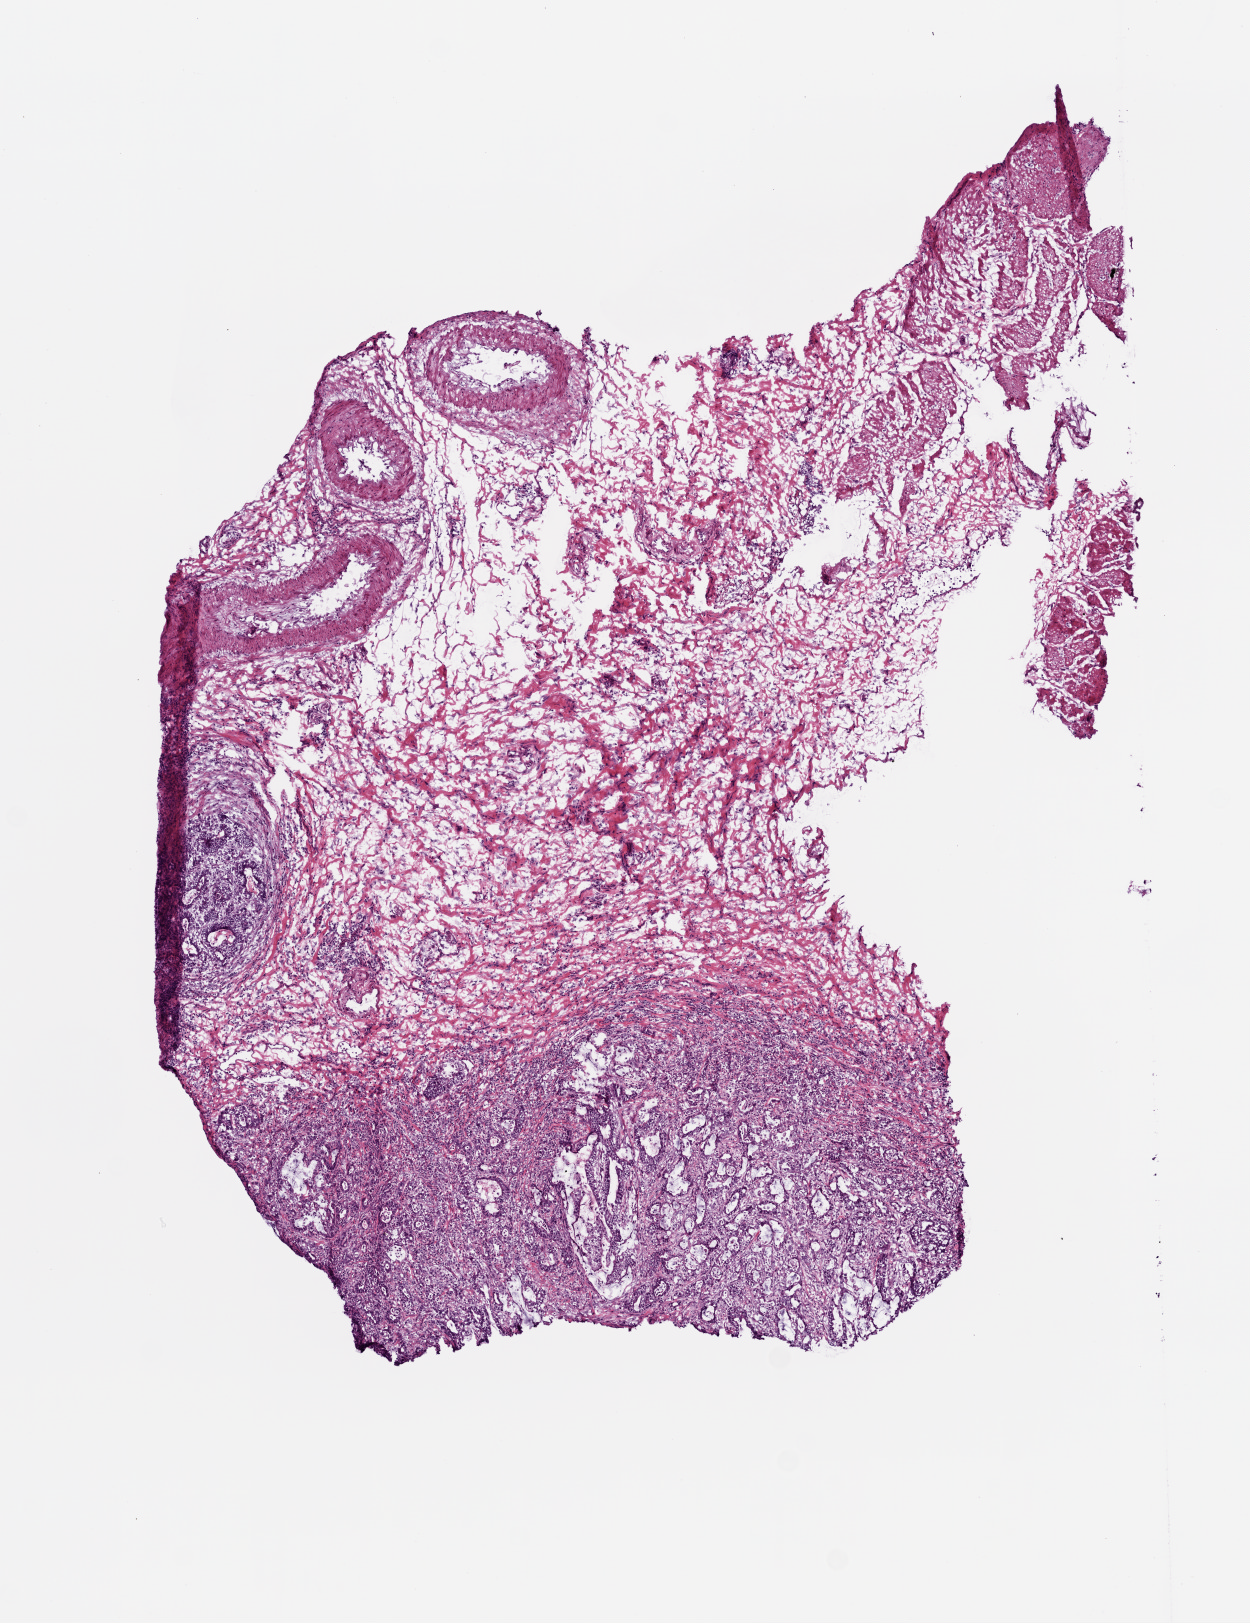
Digitized Hematoxylin and eosin (H&E) stained tissue section (whole slide), low-resolution overview of the scanned area, about 5.0 x 6.5 mm; frozen section from the top of the tissue portion; primary tumour sample from the stomach. Female patient. Composition of this section per pathologist review: tumour cells 50%, tumour nuclei 70%.
Pathologic diagnosis: Adenocarcinoma, intestinal type (gastric antrum).